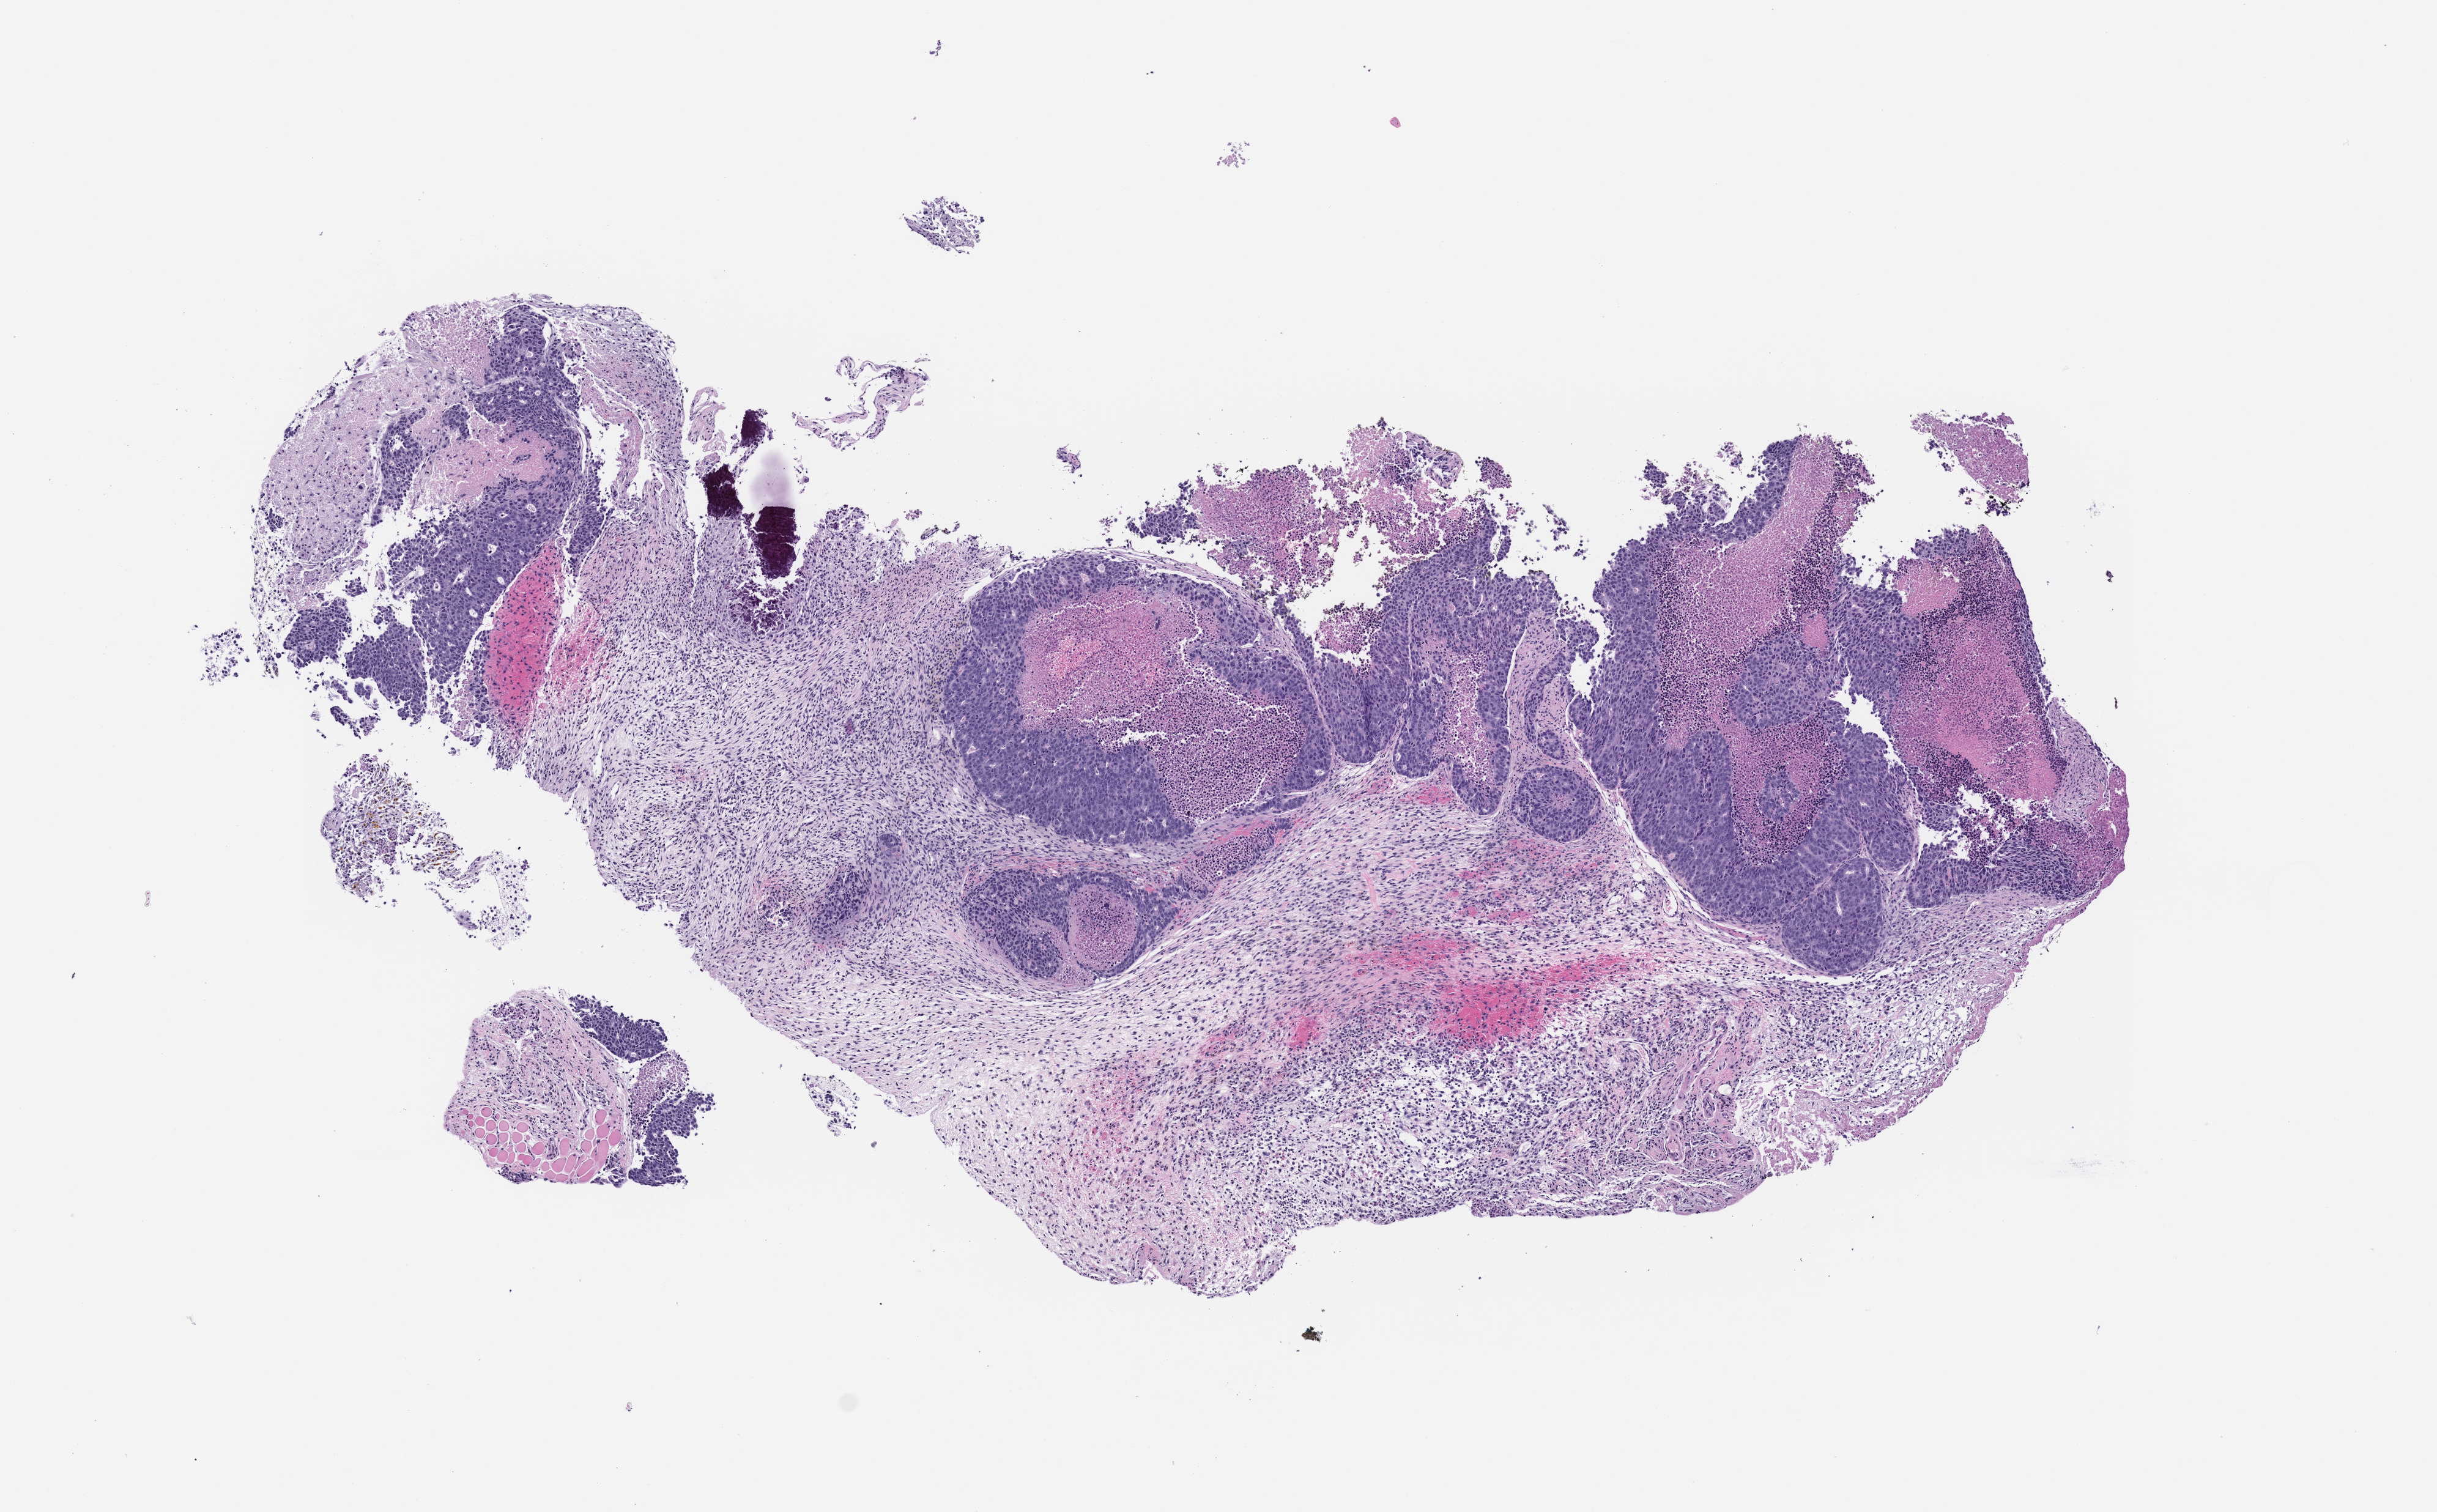
H&E whole-slide image of a patient-derived xenograft (PDX) tumor grown in a mouse, passage 2, whole scanned area (about 8.0 x 5.0 mm) shown as a low-resolution overview, formalin-fixed, paraffin-embedded (FFPE) tissue, tumor site category: colon.
- originating patient diagnosis: Colon Adenocarcinoma